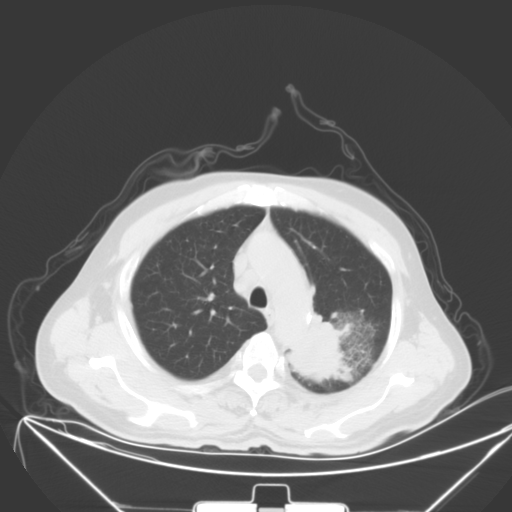
Chest CT, one axial slice. Slice 45 of 64 in the series (ordered by position). 120 kVp. Lung window (W 1500 / L -600 HU). 5 mm slice thickness. 512 × 512 image matrix. Male patient, age 58 years. Case-level facts recorded for this patient, not image findings: clinical TNM (as recorded): T2b N3 M1b; histopathological grade: G3.
Structures marked on this image (rectangle marked by the reading radiologist):
- lung tumour (recorded histology: adenocarcinoma): bounding box (x1, y1, x2, y2) in pixels: (287, 313, 349, 385)